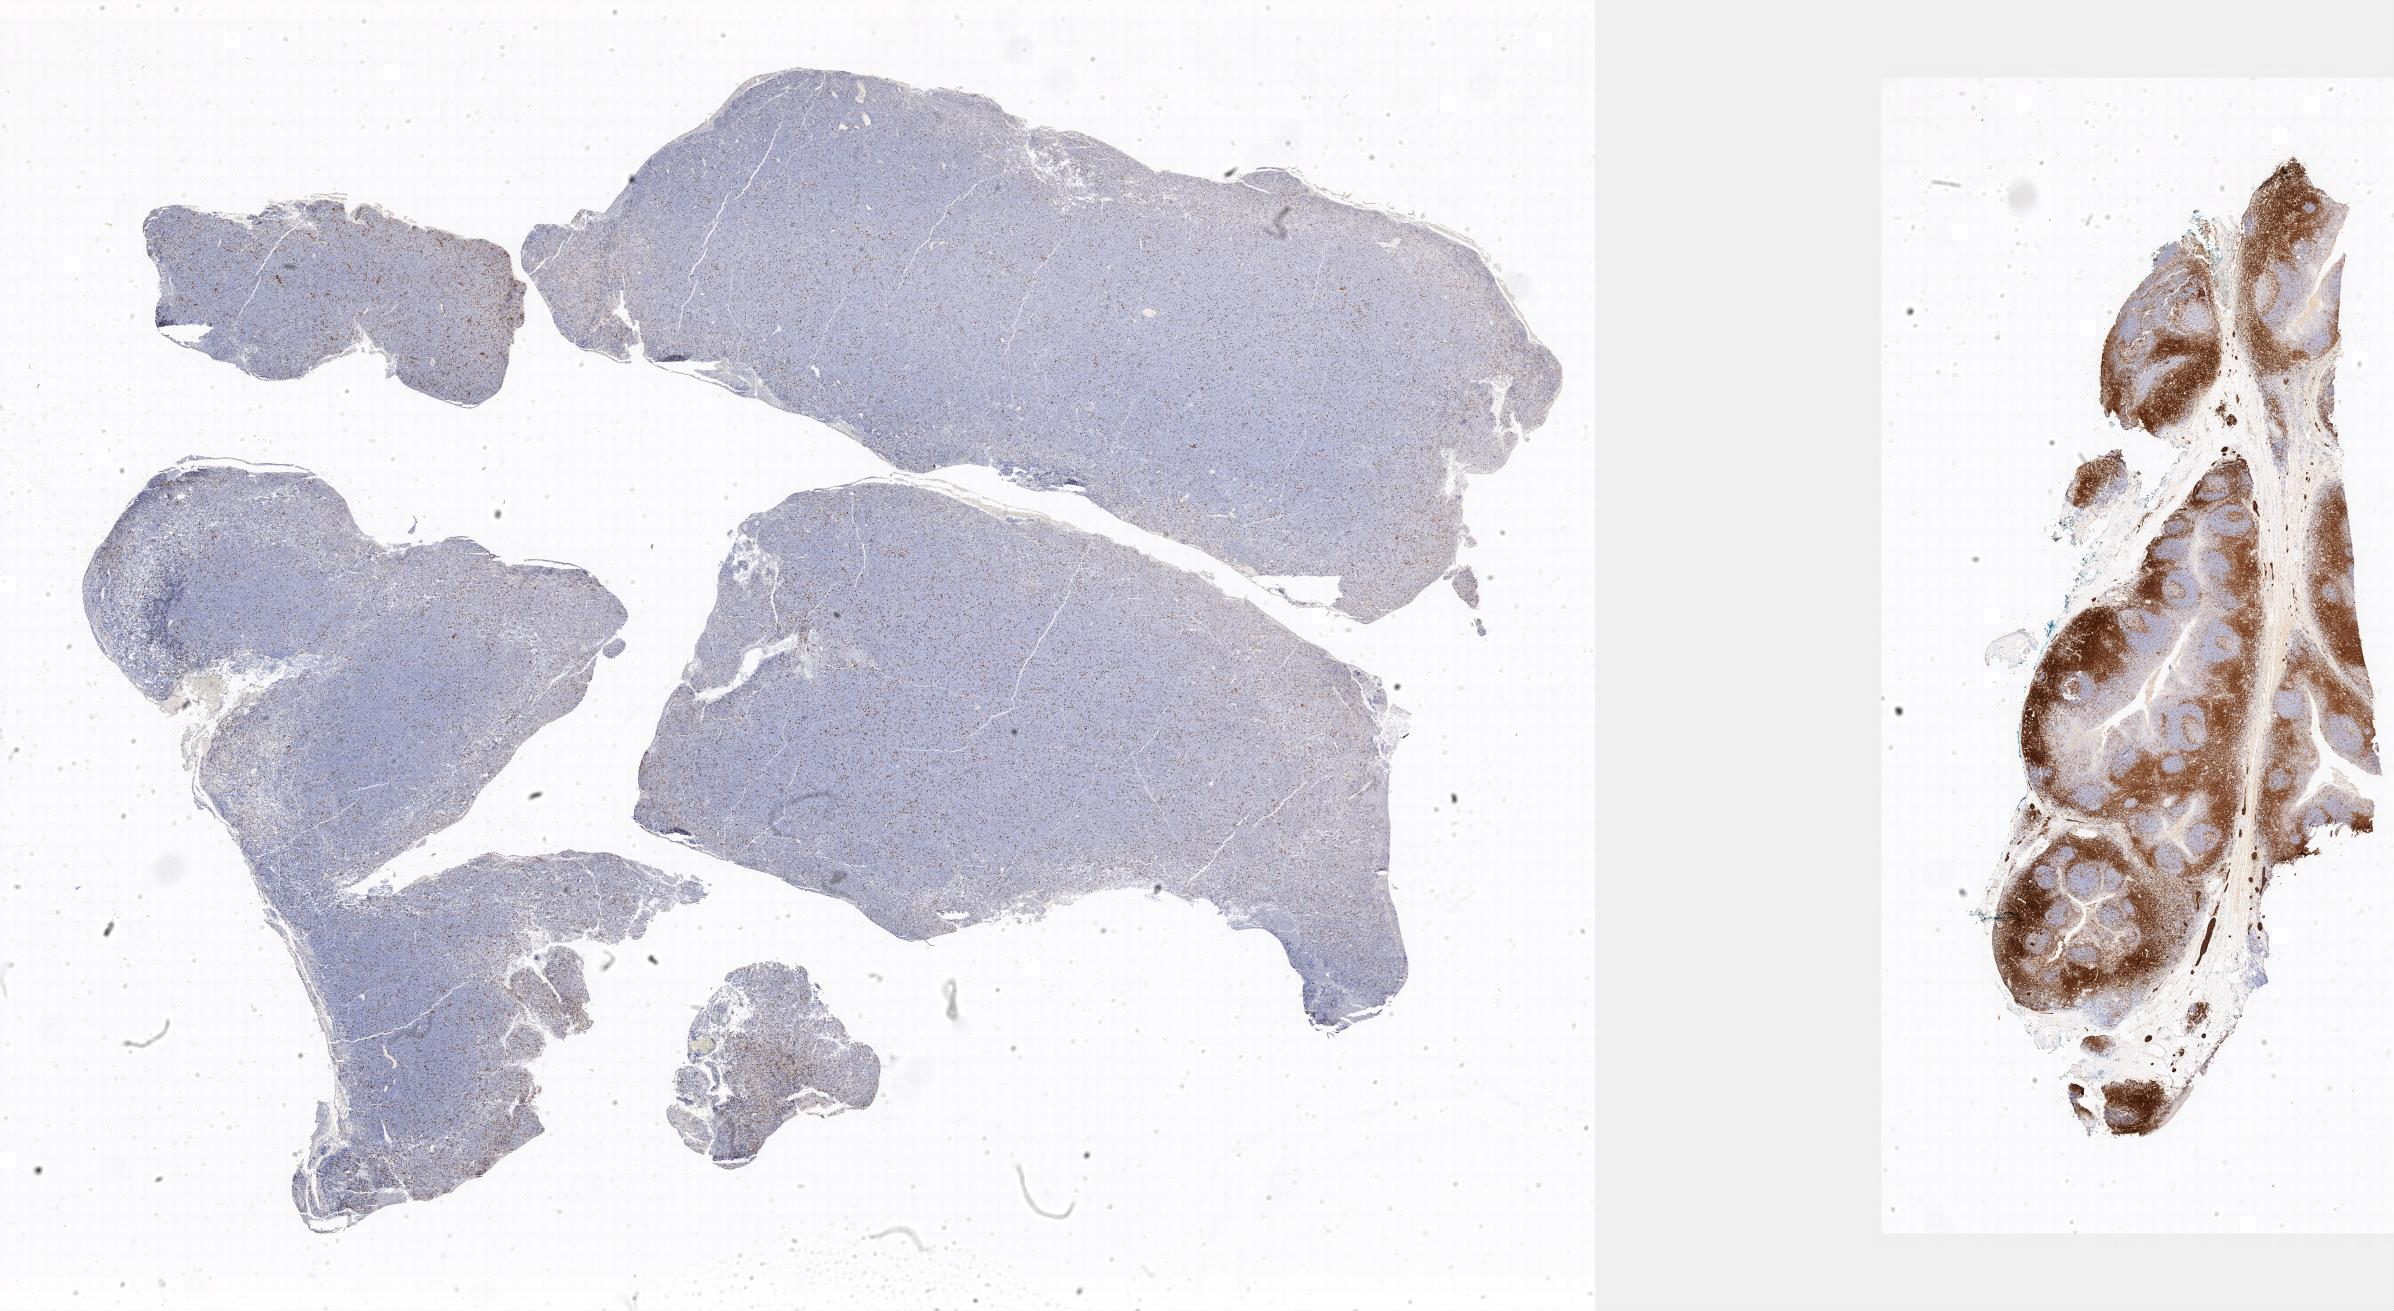
Immunohistochemistry (IHC) whole-slide image stained for CD3, shown as a low-resolution overview of the whole scanned area, tumor tissue, site: peritoneum. Female, age 7 years at initial diagnosis.
• histologic diagnosis: Burkitt lymphoma, NOS